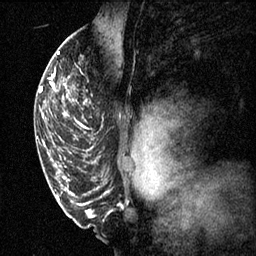
Breast MRI (dynamic contrast-enhanced), one sagittal slice; position 43 of 60 along the scan axis; 3 images stored at this slice position (order not interpretable as contrast timing); 1.5 T; TE 4.2 ms, TR 11.1 ms; 2 mm slice thickness; 256 × 256 image matrix. Patient: female, 50 years.
Structures marked on this image (semi-automatically segmented with operator editing):
- analysis volume of interest (the breast-tissue region the enhancement analysis was run in; not a lesion): box from (x=68, y=68) to (x=103, y=141) px
- tumour enhancement mask (voxels above the 70 % enhancement threshold inside the analysis volume of interest): (x=68, y=76)–(x=92, y=139)